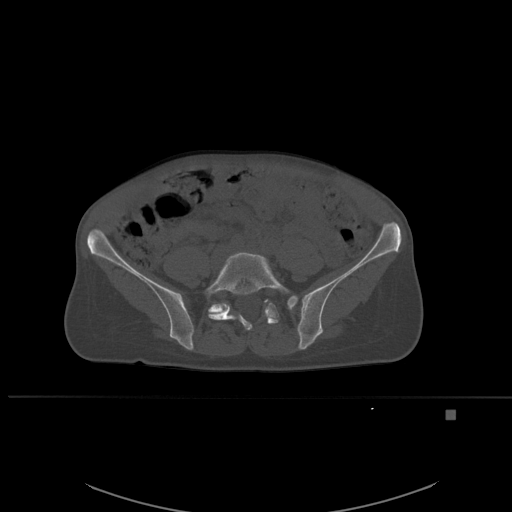
CT including the spine, one axial slice. Position 170 of 537 along the scan axis. Bone window (W 1800 / L 400 HU). 1.5 mm slice thickness. 512 × 512 image matrix, field of view 440 × 440 mm. Patient: female, 45 years. Case-level facts recorded for this patient, not image findings: primary cancer: lung.
Structures marked on this image (semi-automatically segmented with operator editing):
- L5 vertebra: bounding box (x1, y1, x2, y2) in pixels: (204, 252, 298, 330)